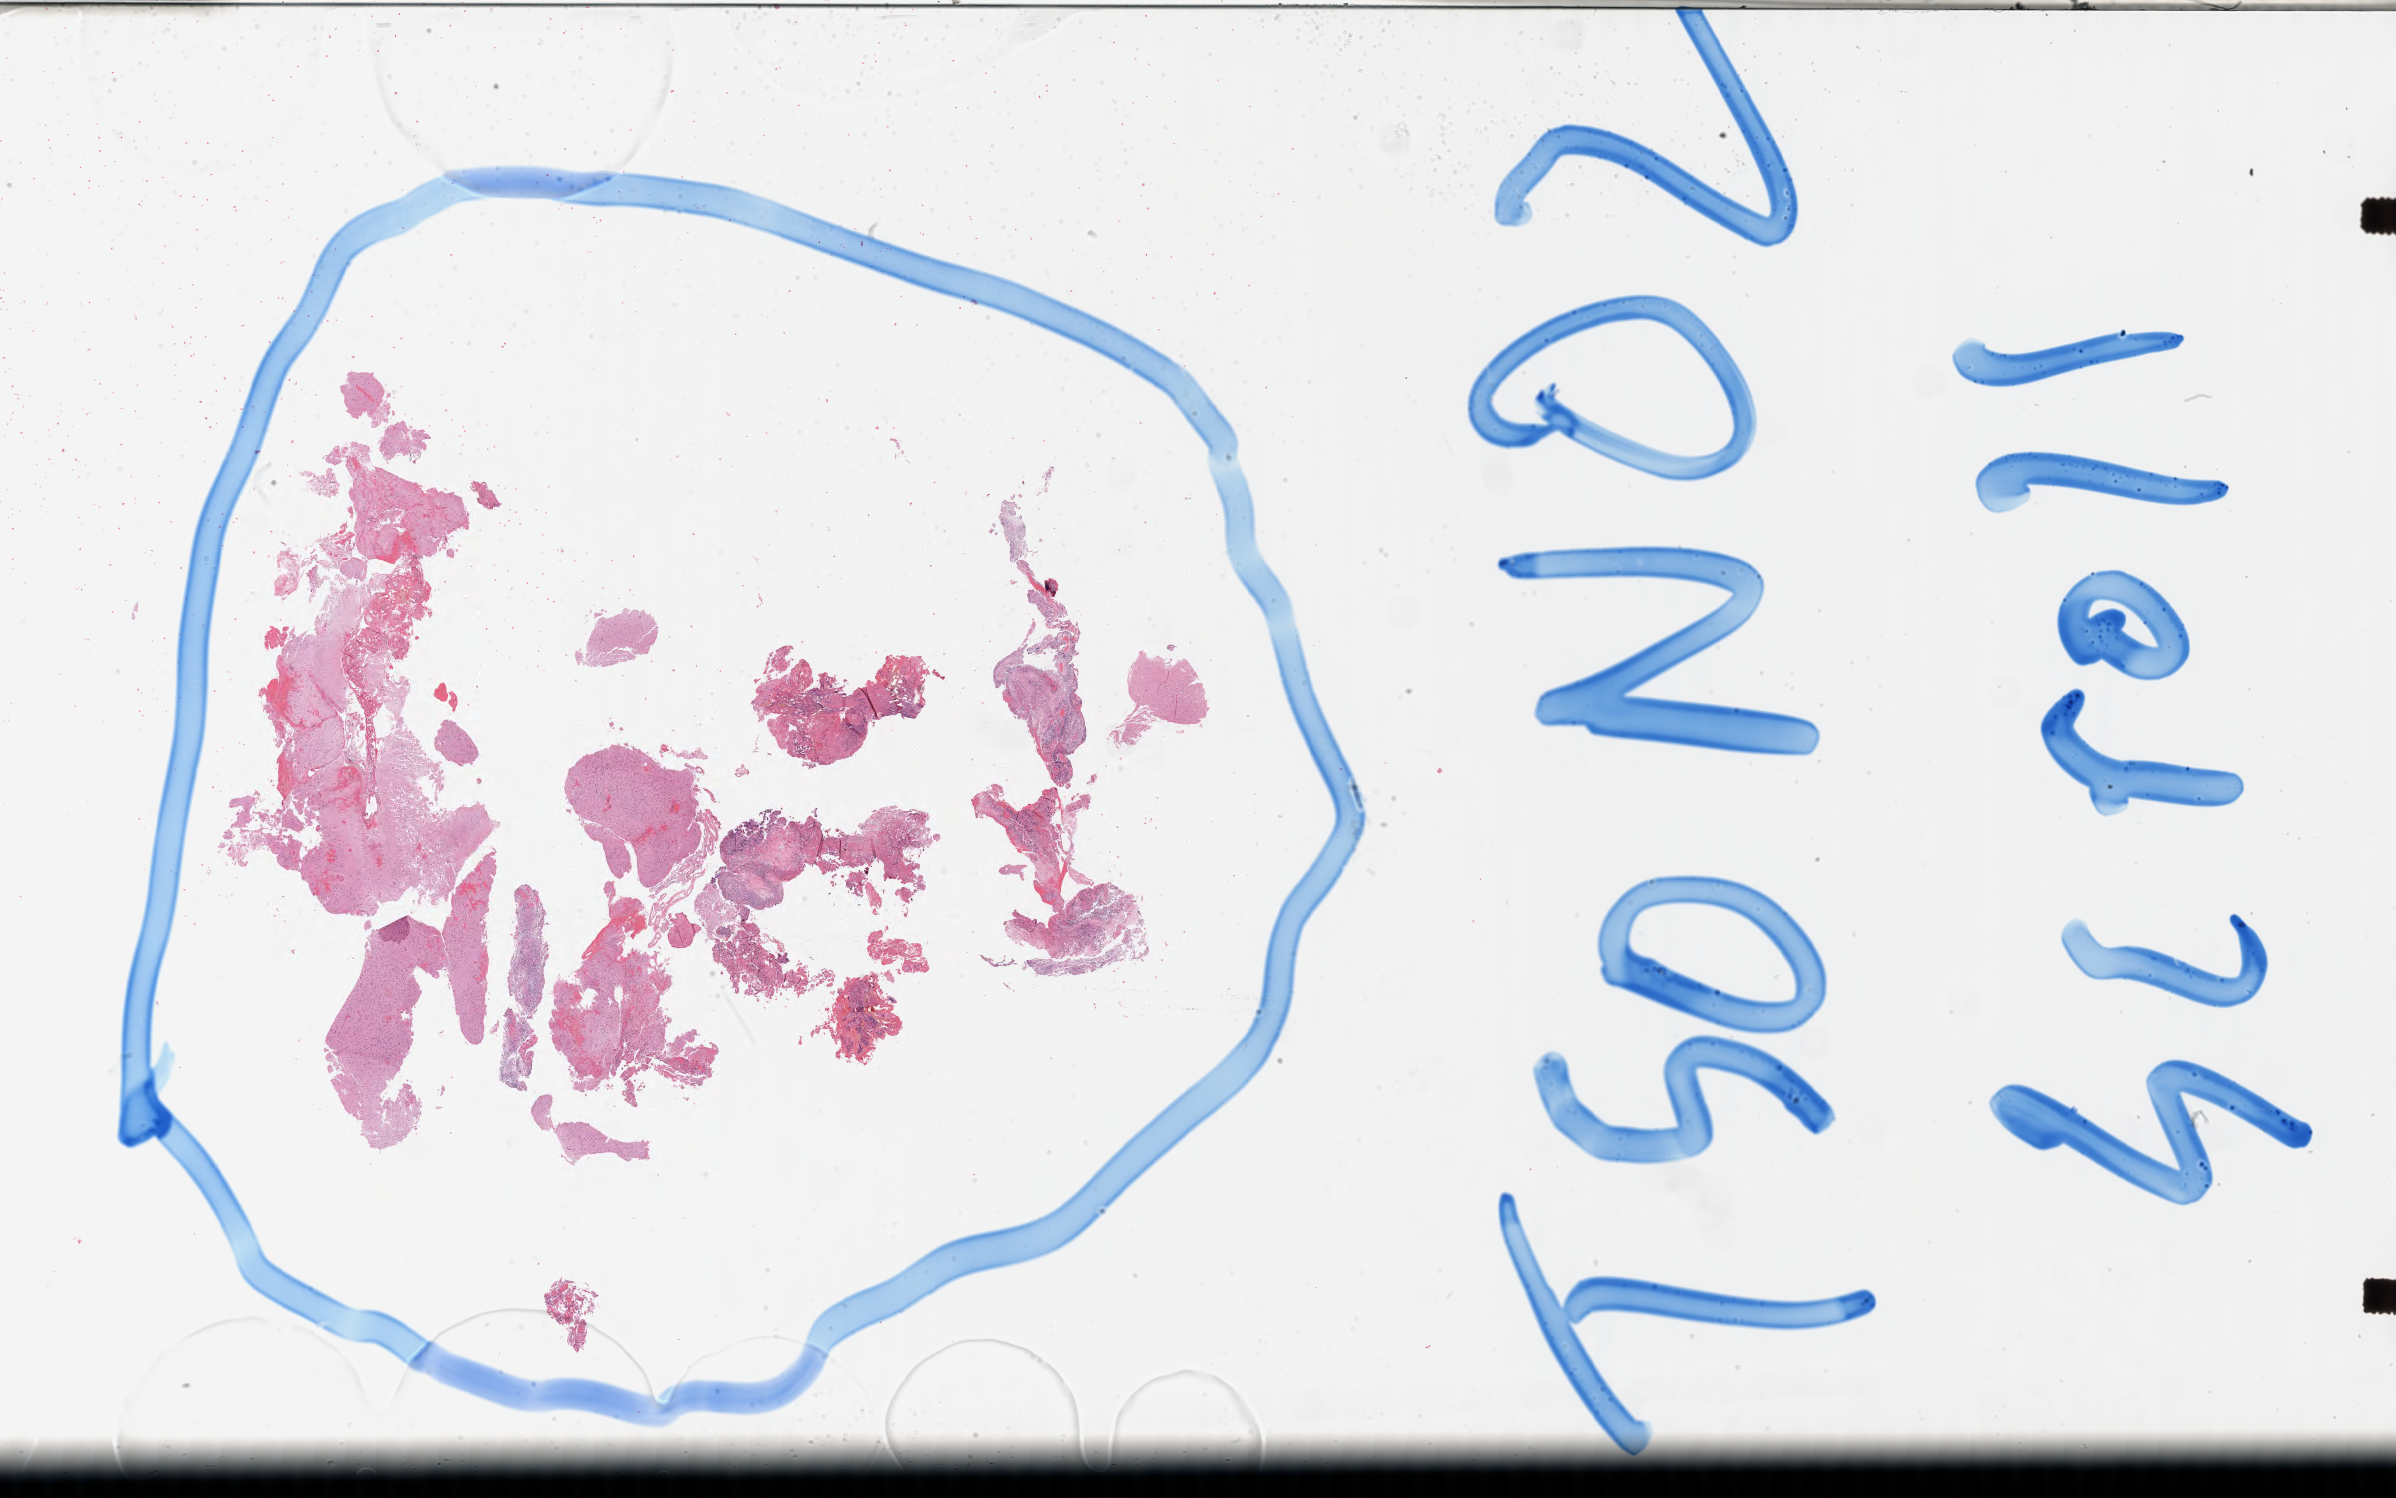
Whole-slide image, H&E stain, shown as a low-resolution overview of the whole scanned area (about 38.7 x 24.2 mm). Formalin-fixed, paraffin-embedded (FFPE) tissue. Specimen: recurrent tumor. Anatomic site: brain. Male, age 59 years at initial diagnosis. Pathologist review of this section (percent, as recorded): tumor cells 31%, tumor nuclei 51%, stromal cells 37%, necrosis 2%, normal cells 30%. Inflammatory infiltration, as recorded: lymphocyte infiltration 0%, monocyte infiltration 0%, neutrophil infiltration 0%.
Patient diagnosis: Glioblastoma, NOS. Section: bottom of the tissue portion.